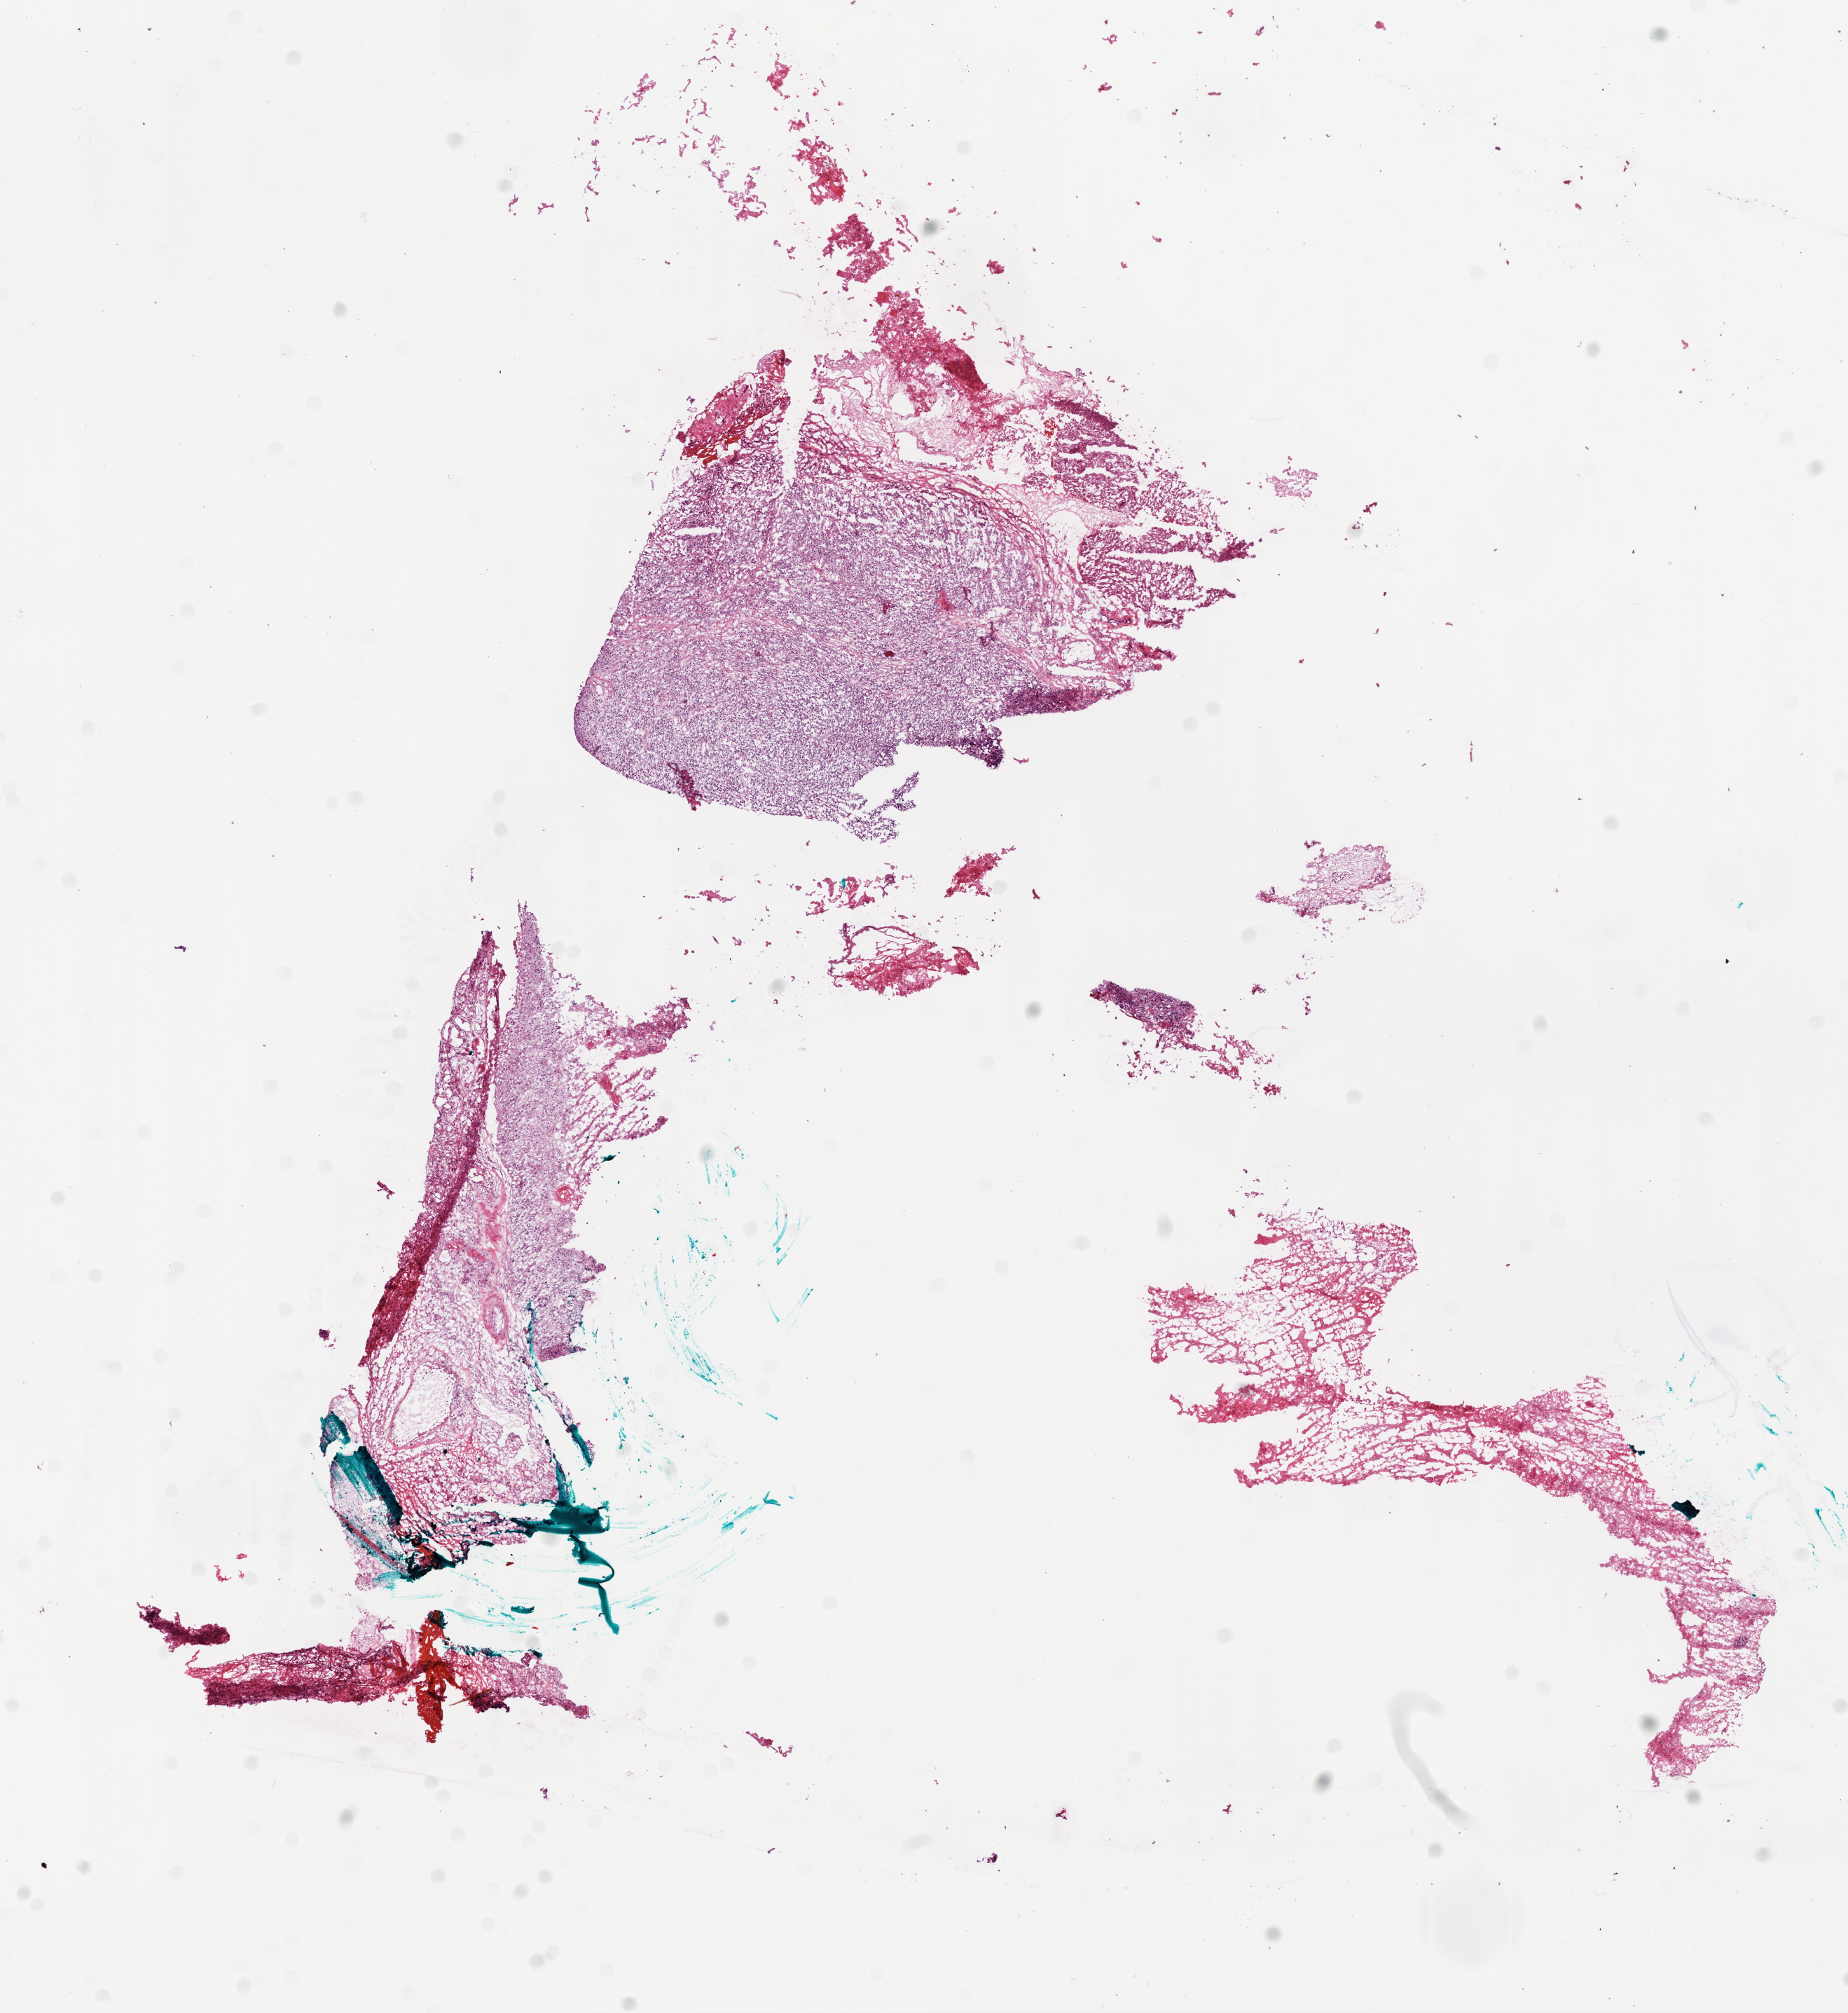
Digitized Hematoxylin and eosin (H&E) stained tissue section (whole slide), low-resolution overview of the scanned area, about 10.6 x 11.6 mm (from a 20x scan). Frozen section. Primary tumour sample from the brain. Patient: male, age at initial diagnosis 74 years. Pathologist review of this section (percent, as recorded): tumour cells 60%, tumour nuclei 95%, normal cells 0%, stromal cells 20%, necrosis 20%.
• diagnosis: Glioblastoma